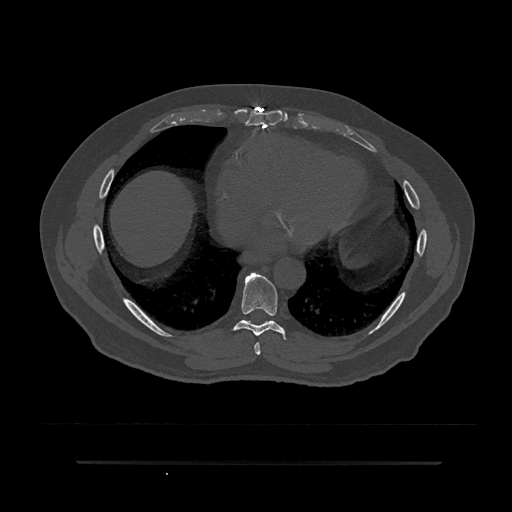
CT including the spine, one axial slice; slice 427 of 797 in the series (ordered by position); reconstruction kernel Br40s/3; 120 kVp; bone window (W 1800 / L 400 HU); 0.5 mm slice thickness; 512 × 512 image matrix, field of view 464 × 464 mm. Male patient, age 59 years. Case-level facts recorded for this patient, not image findings: primary cancer: bile ducts.
Structures marked on this image (semi-automatically segmented with operator editing):
- T7 vertebra: box from (x=254, y=342) to (x=261, y=355) px
- T8 vertebra: (x=232, y=272)–(x=286, y=340)